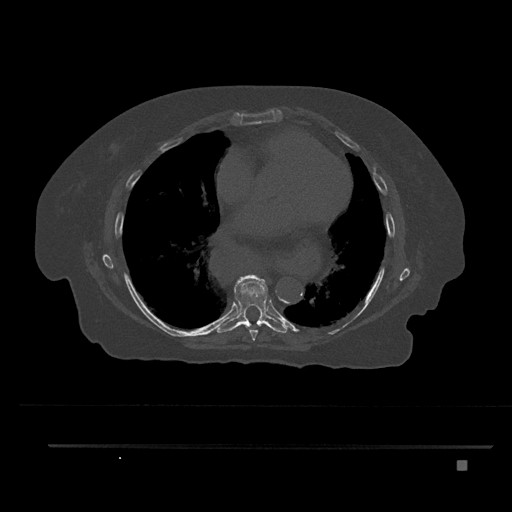
CT including the spine, one axial slice. Slice 457 of 797 in the series (ordered by position). Reconstruction kernel Br40s/3. 120 kVp. Bone window (W 1800 / L 400 HU). 0.5 mm slice thickness. 512 × 512 image matrix. Patient: female, 76 years. Case-level facts recorded for this patient, not image findings: primary cancer: lung; vertebrae with lytic lesions (as recorded): T11, L3.
Outlined on this slice (semi-automatic segmentation, software-assisted and operator-edited):
- T7 vertebra: bounding box (x1, y1, x2, y2) in pixels: (249, 328, 258, 341)
- T8 vertebra: (217, 275, 287, 333)